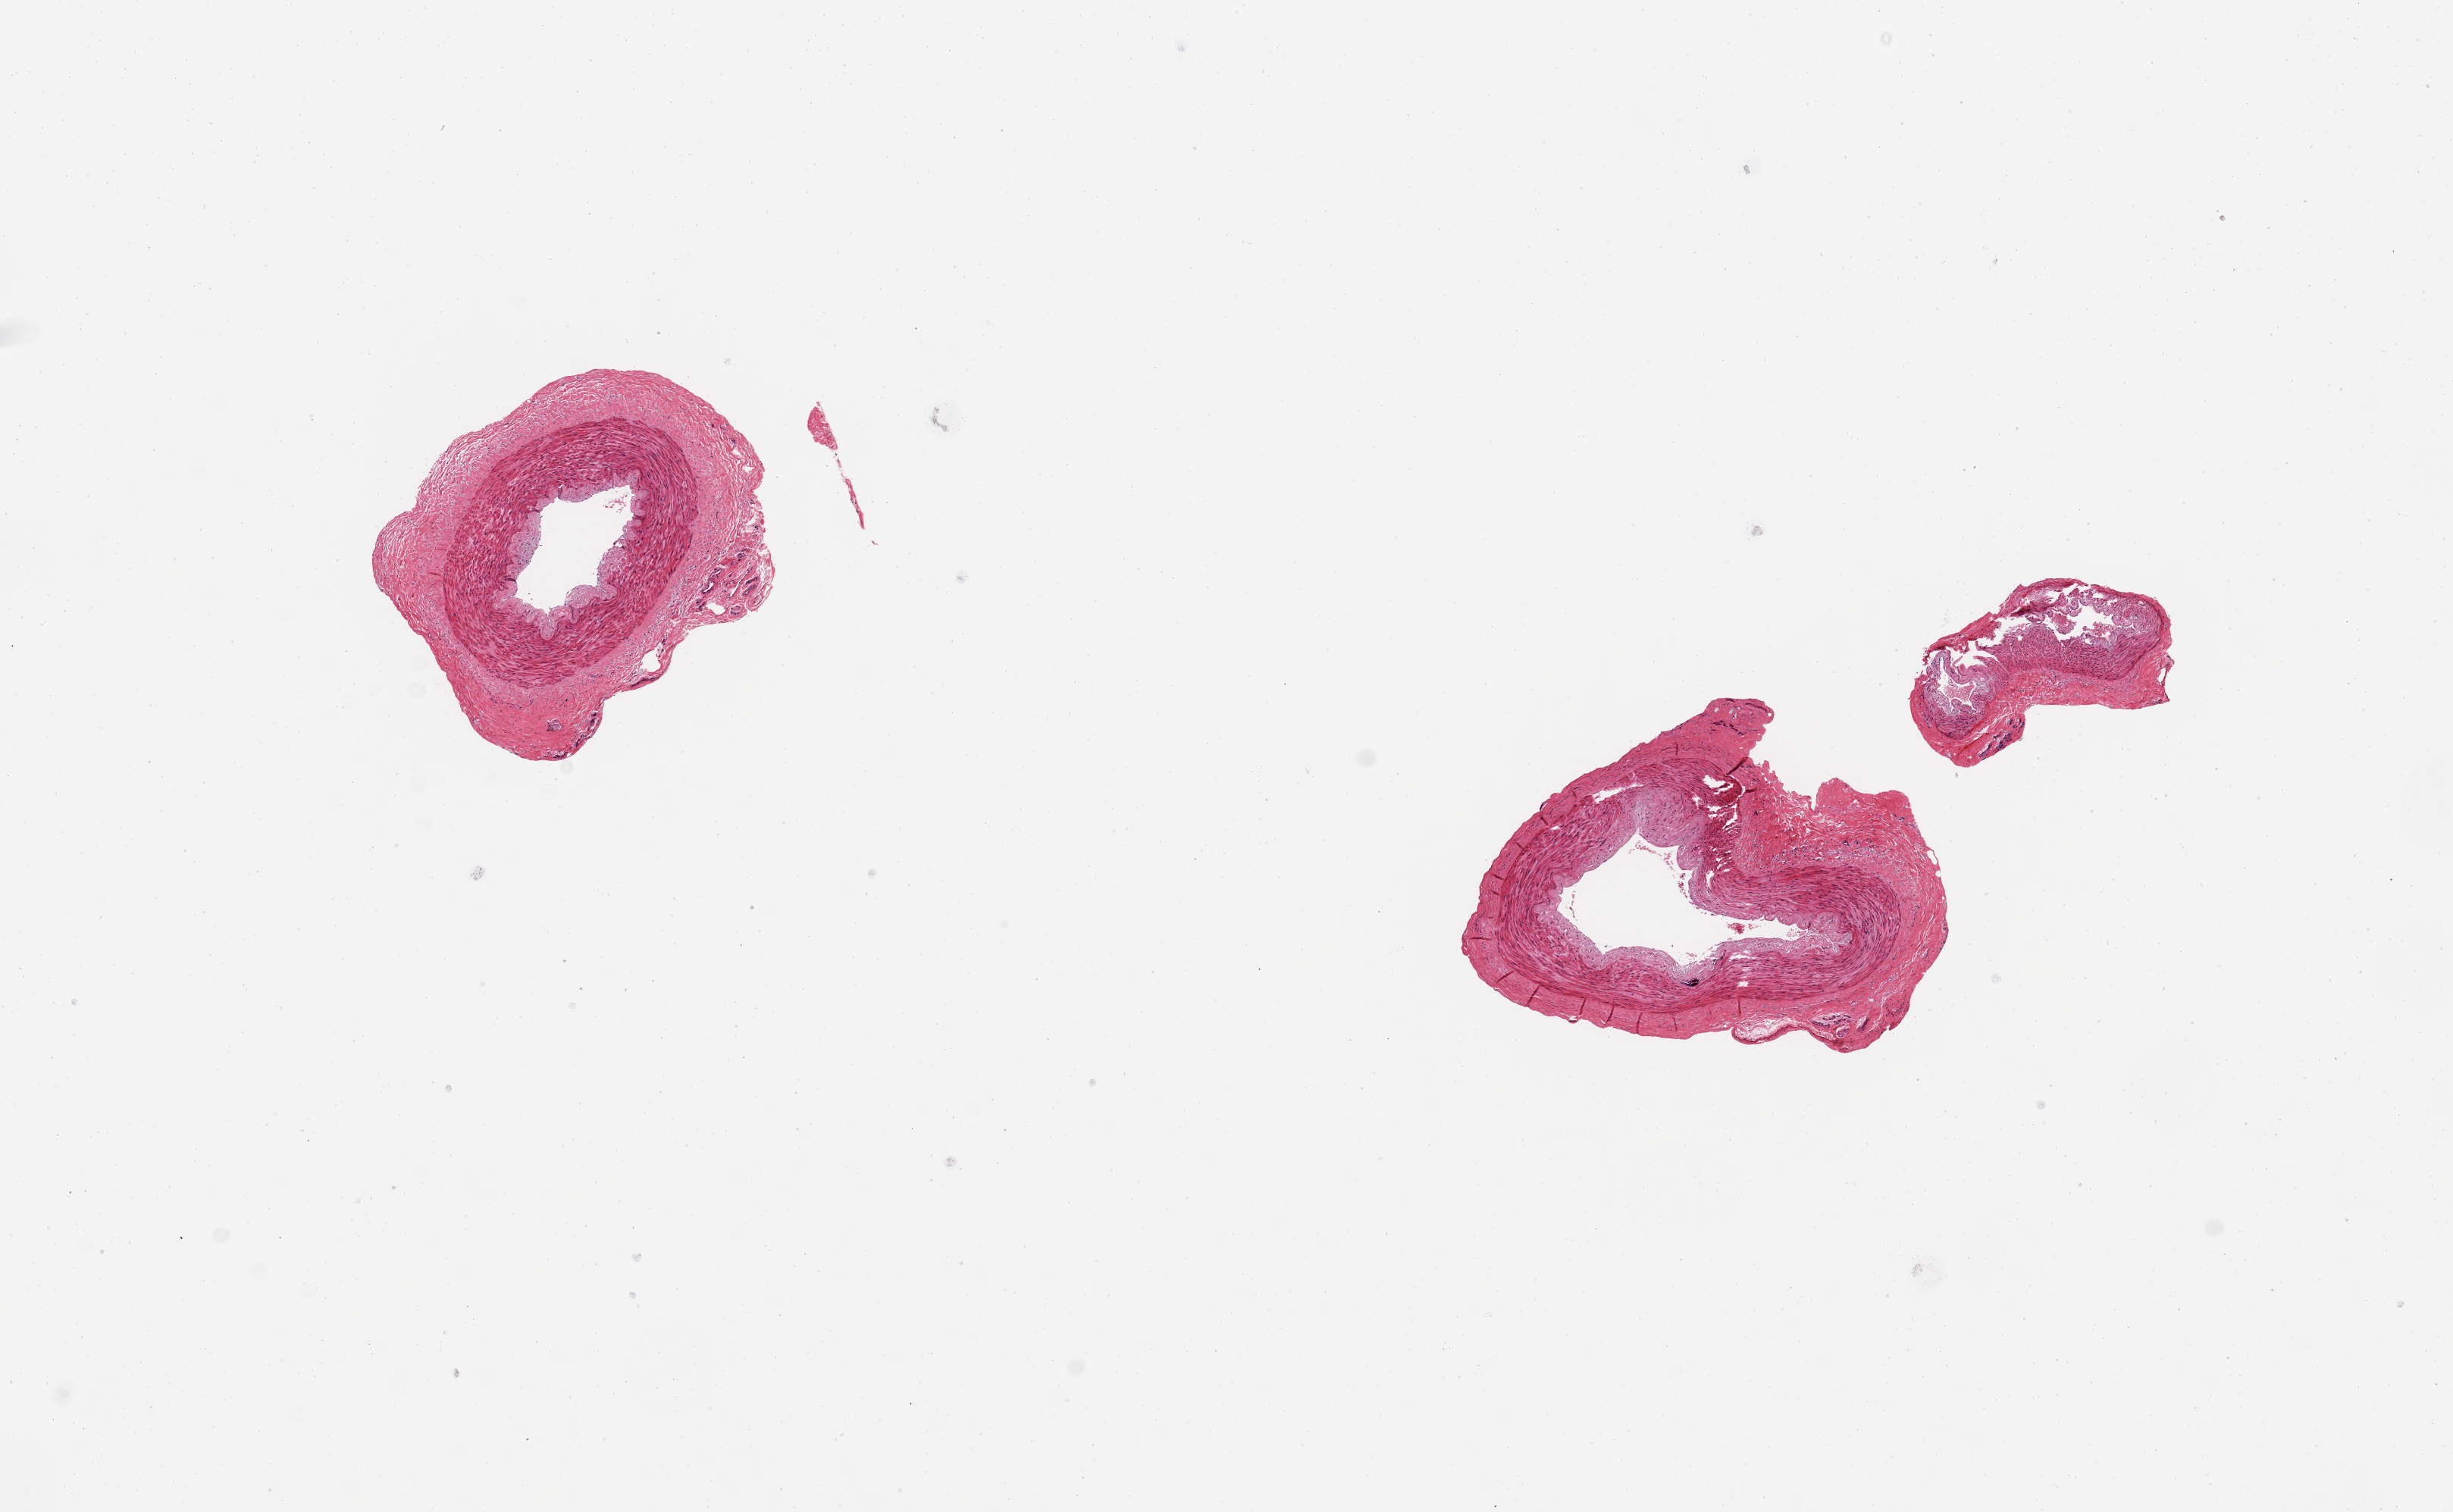
Digitized H&E-stained section, low-resolution overview of the scanned area, about 12.8 x 7.9 mm (slide scanned at 20x); PAXgene-fixed paraffin-embedded (PFPE) section; target tissue: tibial artery; tissue donor sample. Donor: female.
Review note (as recorded): 2 aliquots, ~2mm d. Good clean specimens.